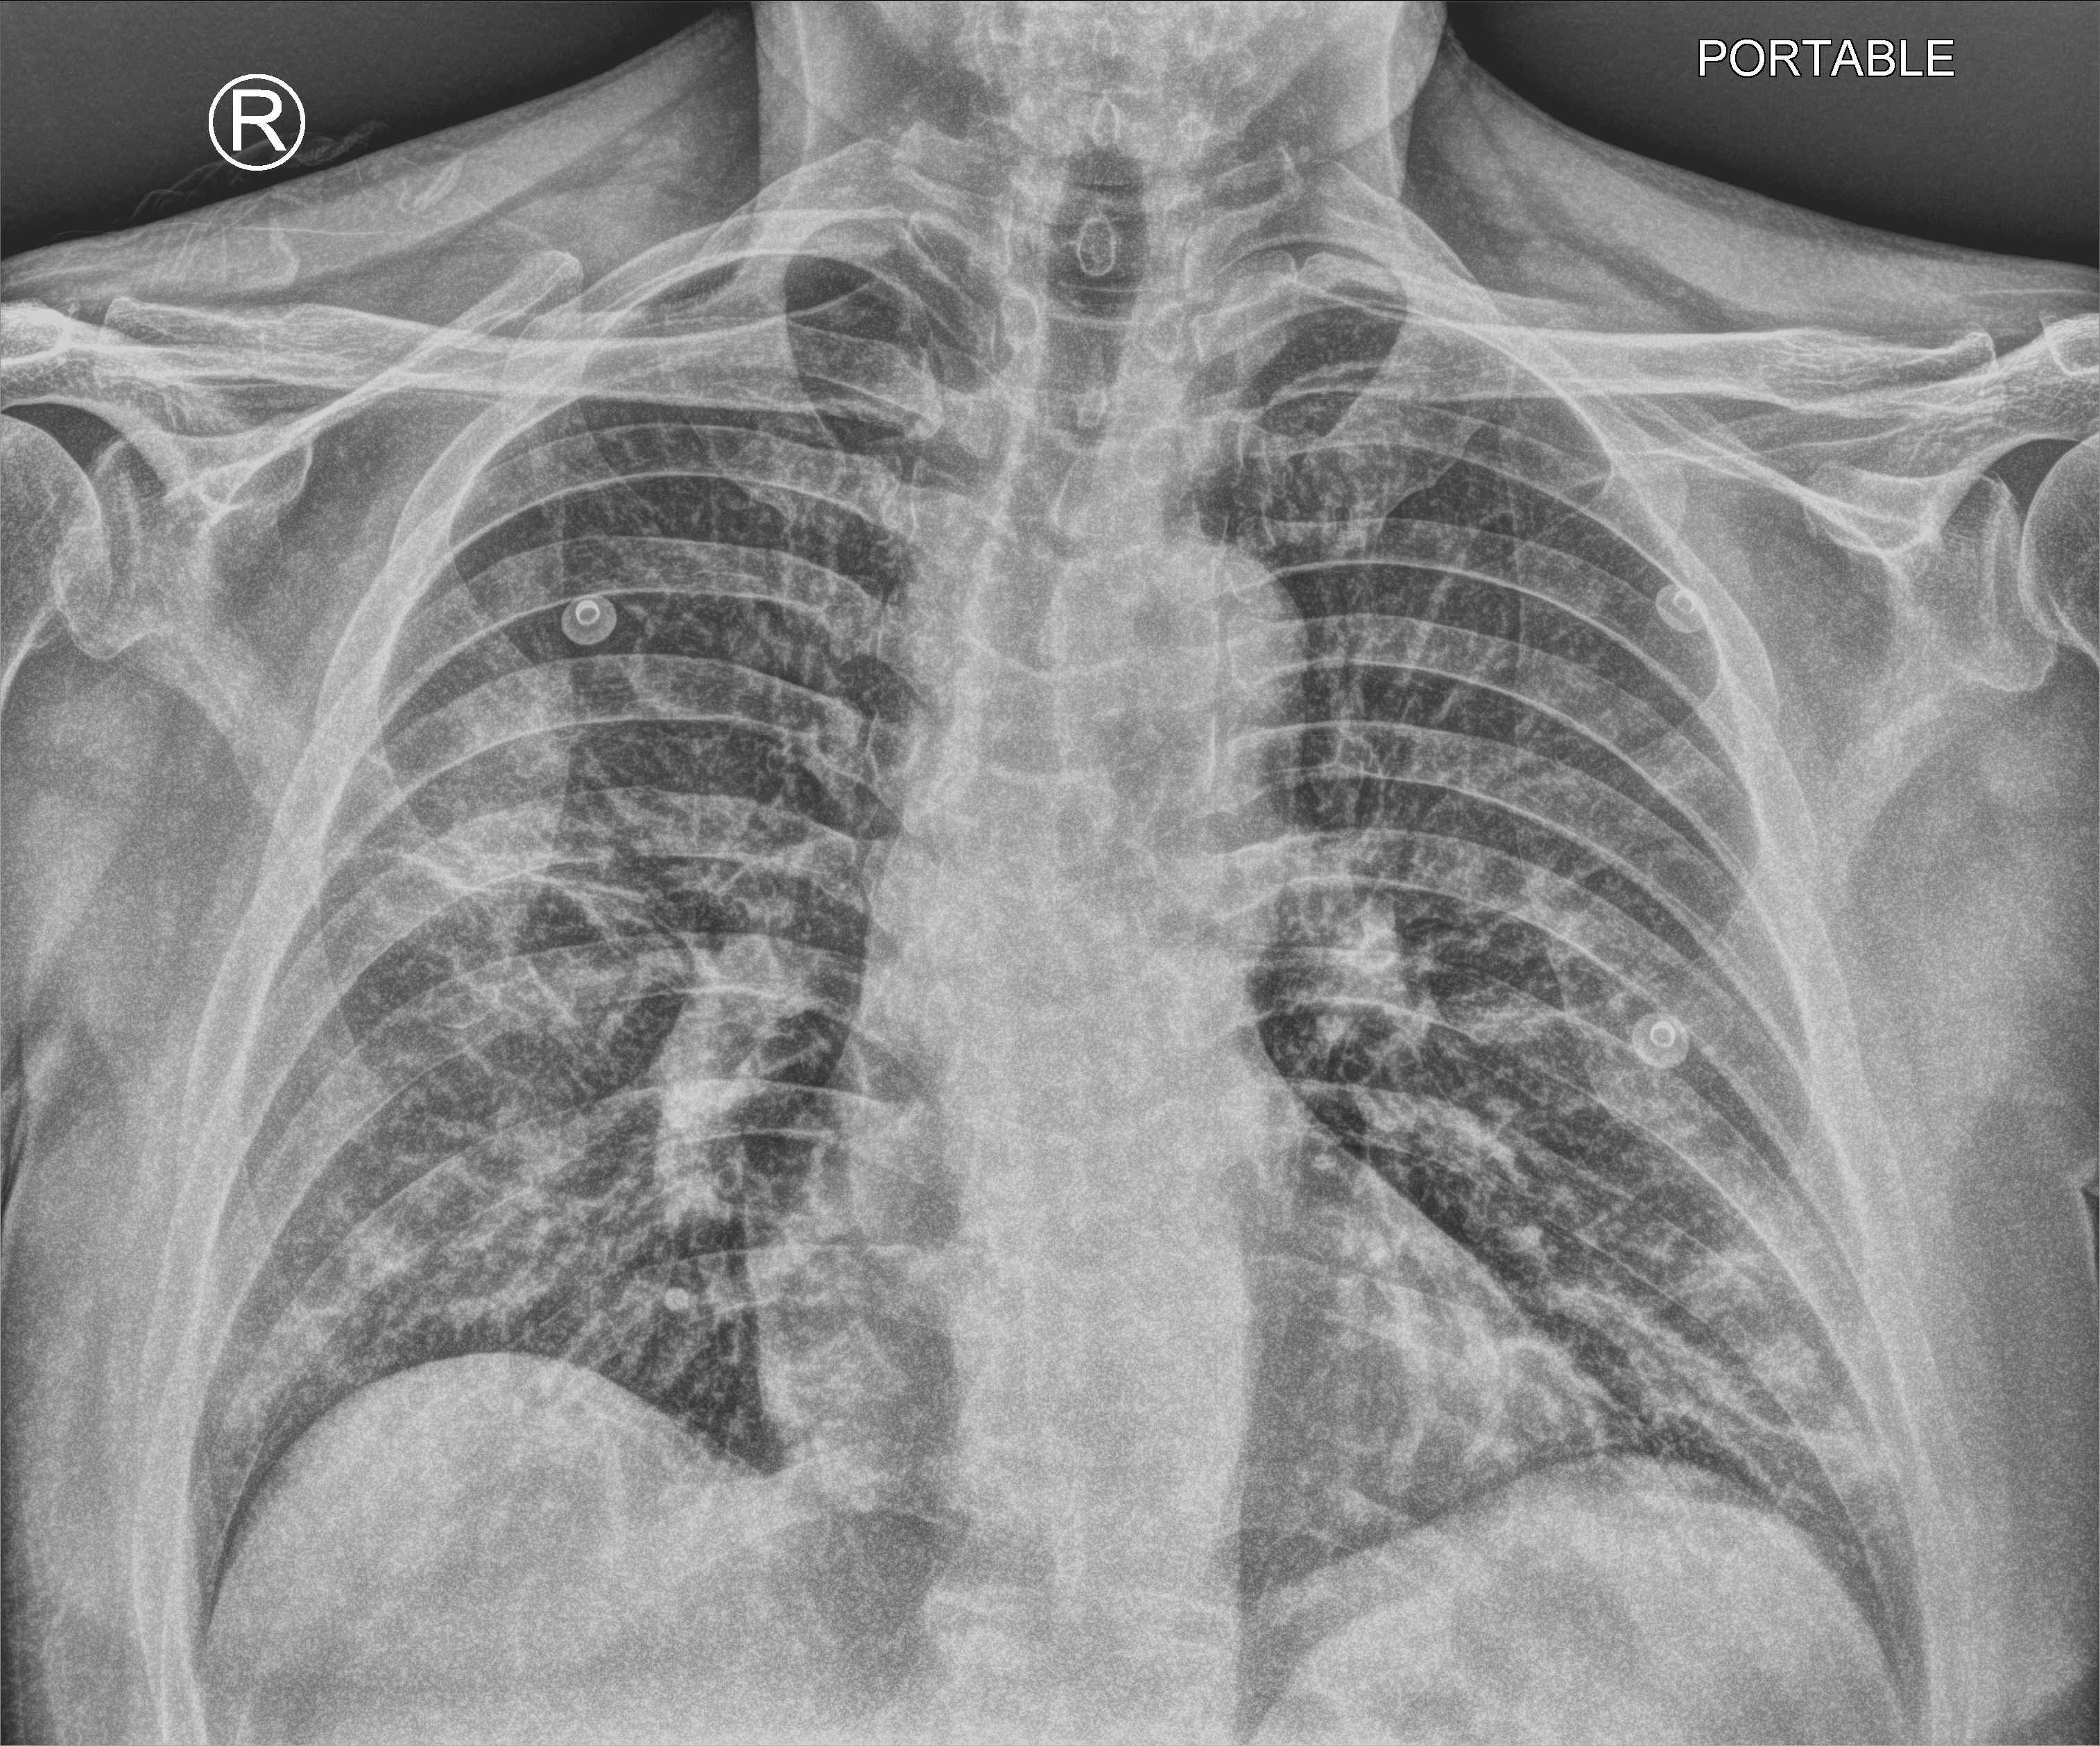
Bedside chest radiograph (computed radiography); anteroposterior (AP) projection. Male patient hospitalised with COVID-19, age 18–59 years.
Hospital-stay facts (about this admission, not read from this image; timing relative to this image not recorded):
- other chronic lung disease (admission record): no
- mechanically ventilated during this hospital stay: no